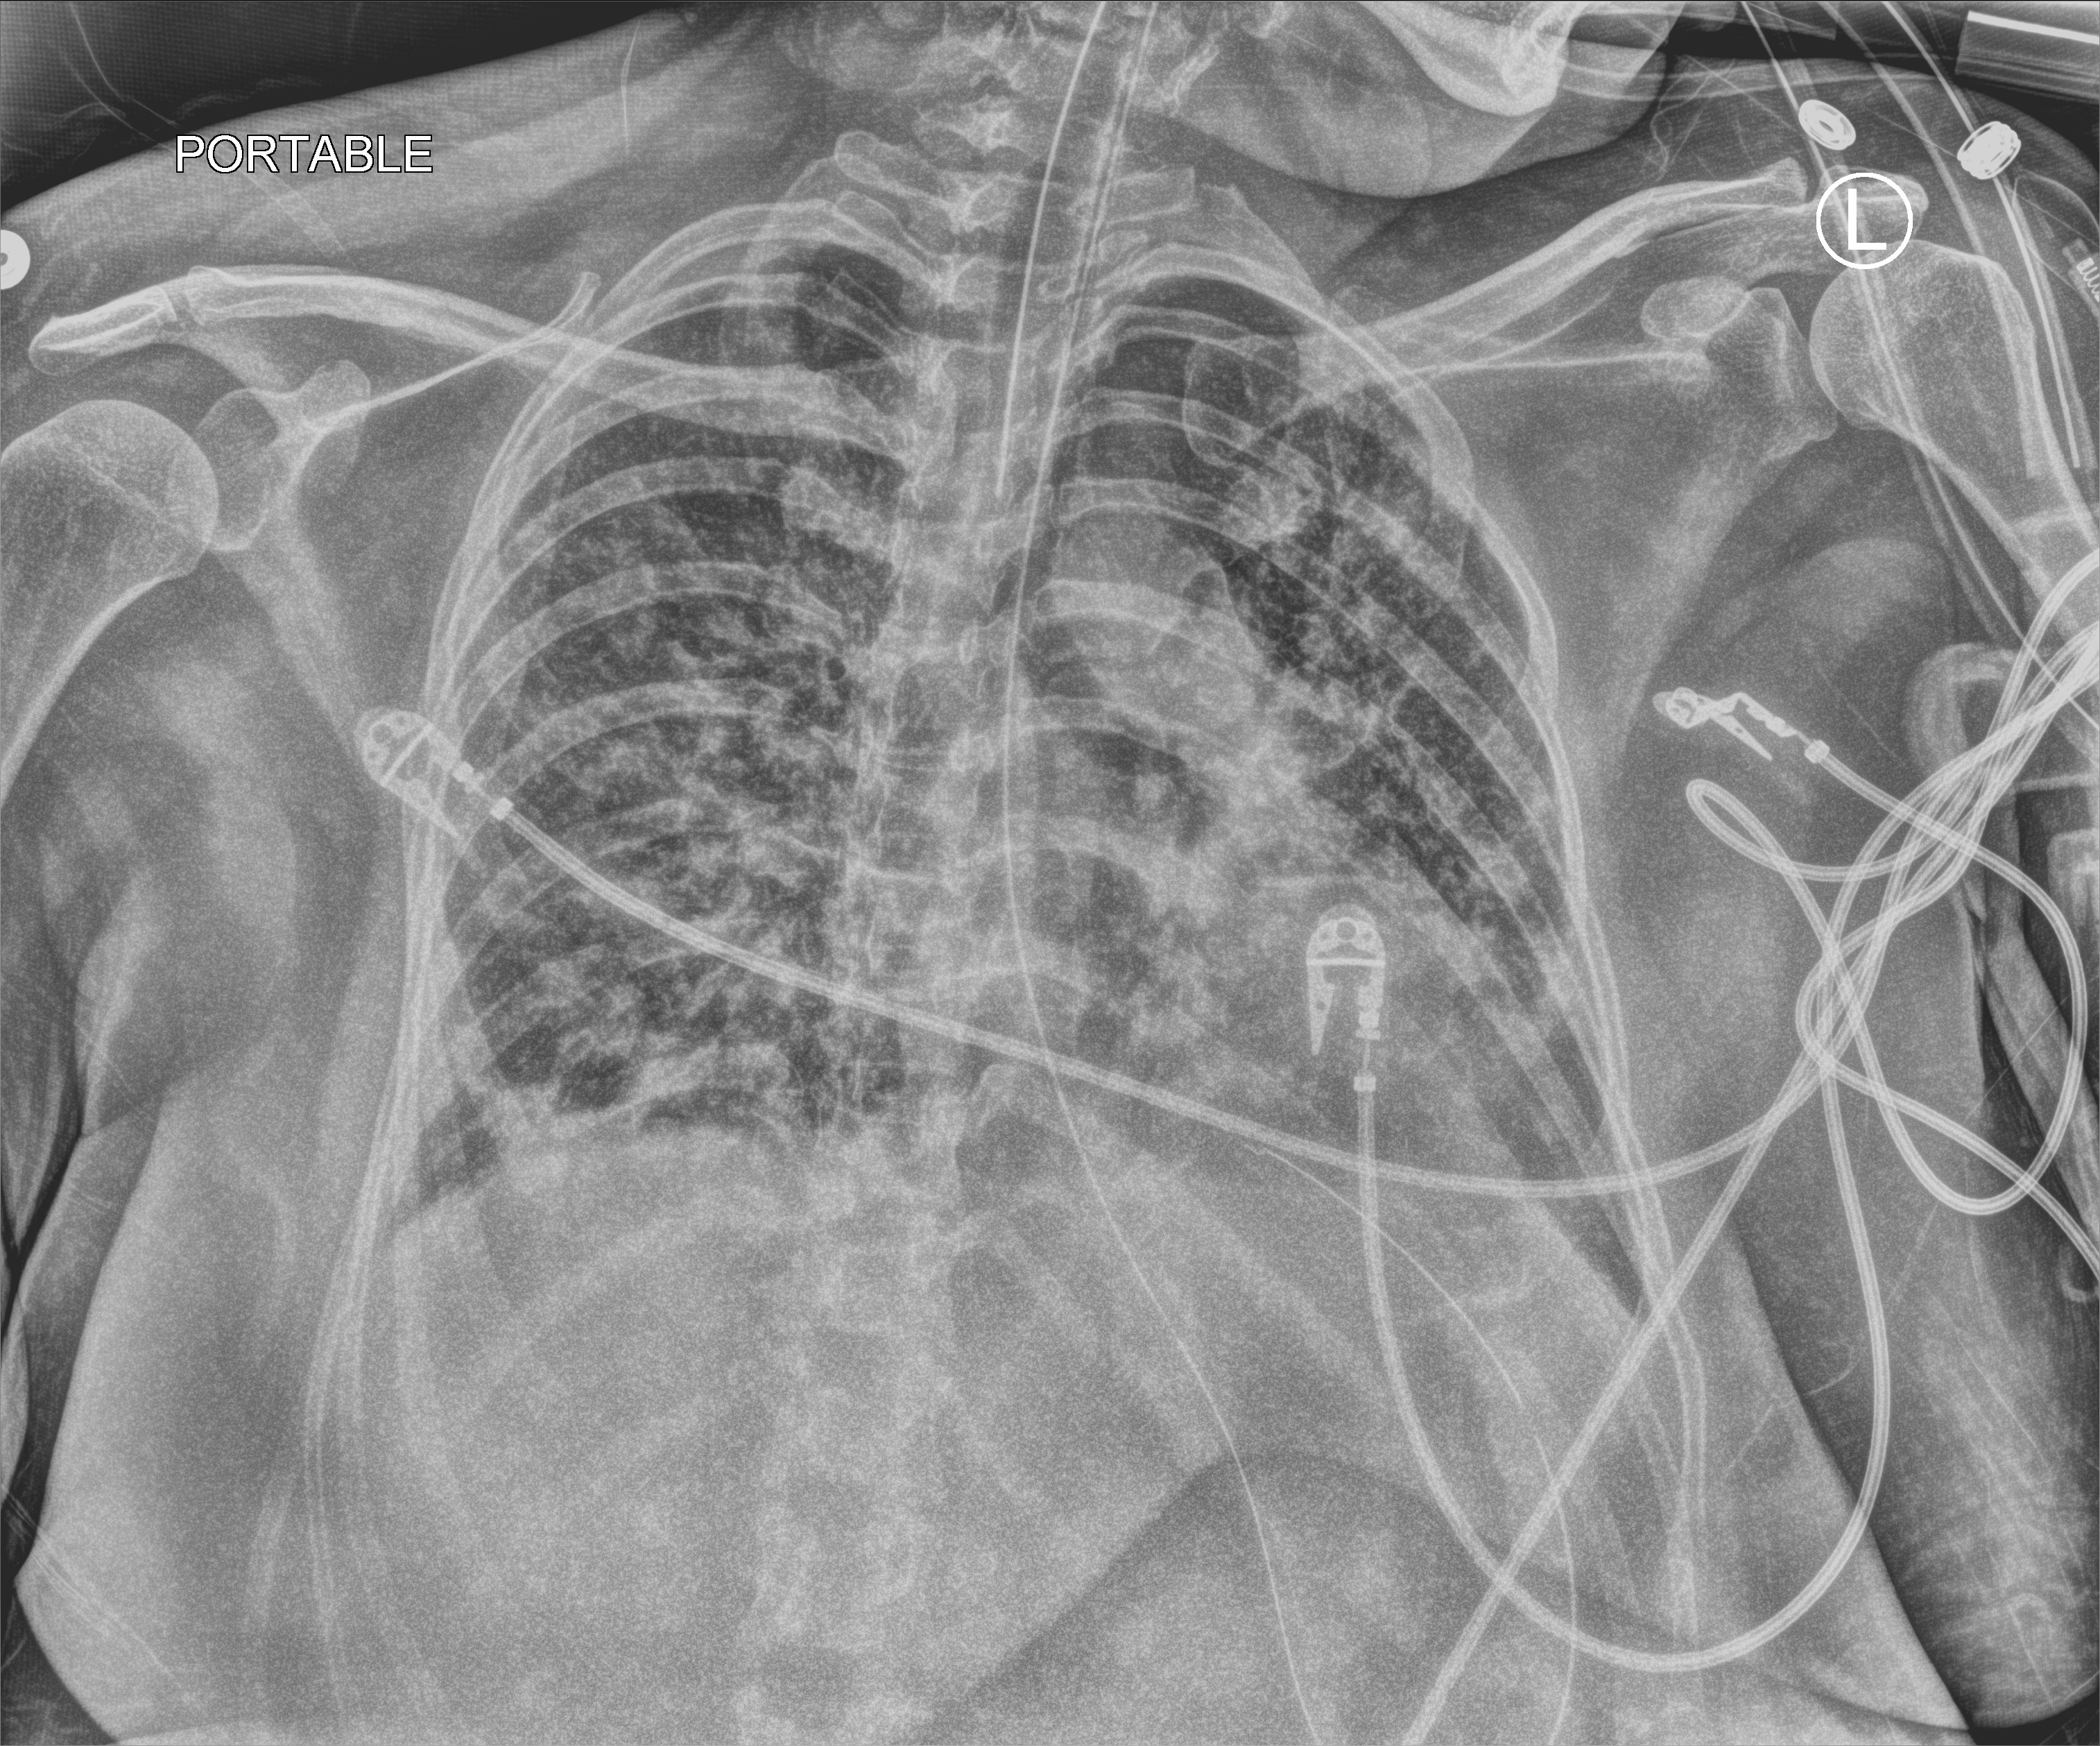
Chest X-ray (portable), anteroposterior (AP) projection. Adult patient hospitalised with COVID-19, age 18–59 years.
Admission-level facts for this patient (not findings on this image; timing relative to this image not recorded): length of hospital stay: 10 days; admitted to intensive care during this hospital stay: yes.